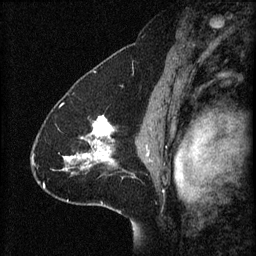
Breast MRI (dynamic contrast-enhanced), one sagittal slice; position 43 of 60 along the scan axis; 3 images stored at this slice position (order not interpretable as contrast timing); 1.5 T; TE 4.2 ms, TR 8.2 ms; 2 mm slice thickness; 256 × 256 image matrix, field of view 200 × 200 mm. Female patient, age 41 years.
Structures marked on this image (semi-automatic segmentation, software-assisted and operator-edited):
- analysis volume of interest (the breast-tissue region the enhancement analysis was run in; not a lesion): bounding box <61,116,124,179> (left, top, right, bottom; pixels)
- tumour enhancement mask (voxels above the 70 % enhancement threshold inside the analysis volume of interest): <64,116,116,169>